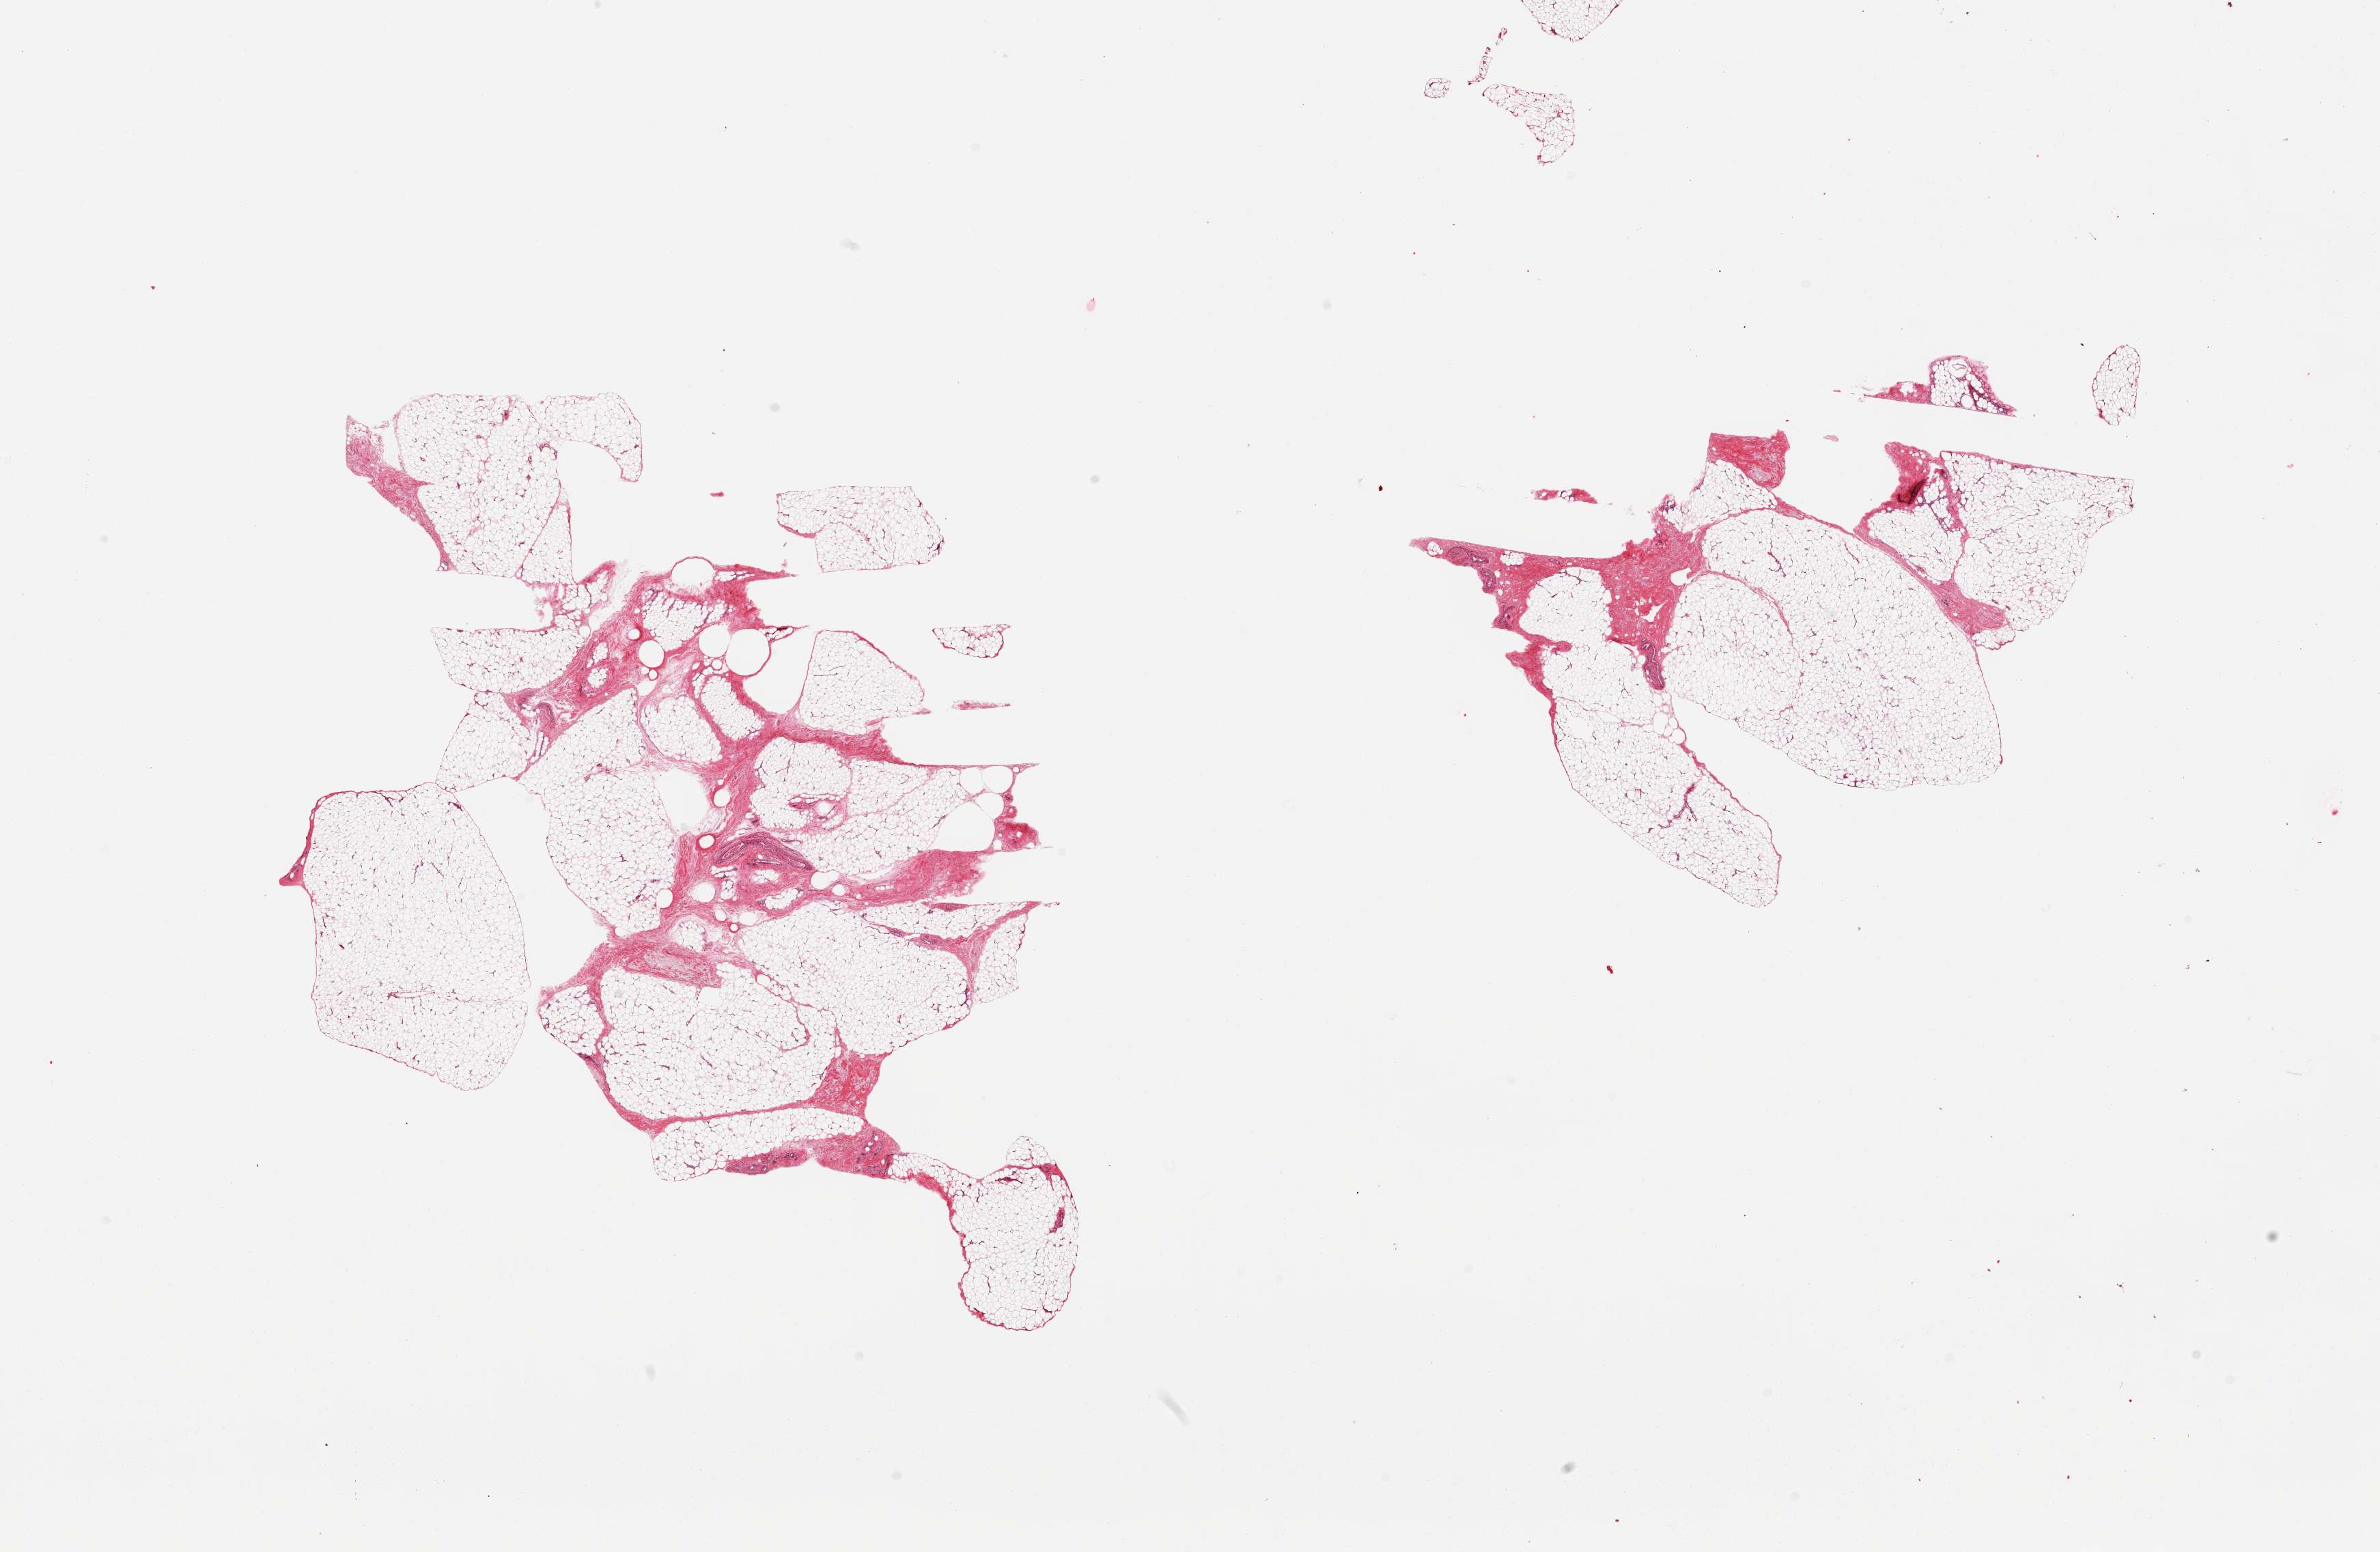
Whole-slide image, H&E stain — a low-resolution overview of the entire scanned area, about 27.6 x 18.0 mm (slide scanned at 20x). PAXgene-fixed, paraffin-embedded tissue. Sampled site (target tissue): adipose tissue. Donor tissue sample. Male donor.
* pathologist's review note for this sample: 2 pieces; ~15% fibrovascular tissue